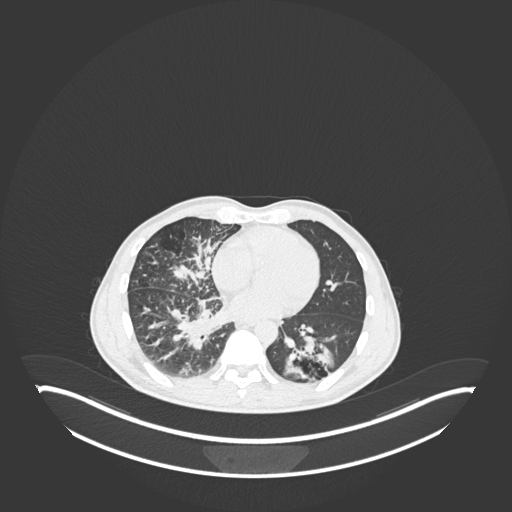
Chest CT, one axial slice. Slice 95 of 237 in the series (ordered by position). Lung window (W 1500 / L -600 HU). 512 × 512 image matrix, field of view 500 × 500 mm. Patient: male, 49 years. From the clinical record (not read from this slice): clinical TNM (as recorded): T2b N1 M0.
Annotated regions visible in this slice (bounding box drawn by a radiologist):
- lung tumour (recorded histology: adenocarcinoma): bounding box (x1, y1, x2, y2) in pixels: (281, 326, 339, 382)